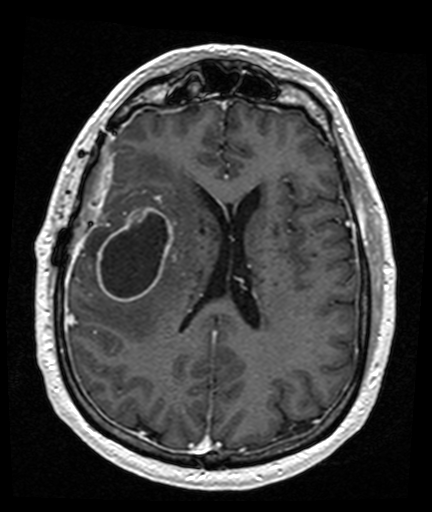
Brain MRI from a brain-tumour surgery series, one axial slice; slice 67 of 176 in the series (ordered by position); T1-weighted post-contrast; 1 mm slice thickness; 432 × 512 image matrix, field of view 194 × 230 mm. From the clinical record (not read from this slice): histopathology: Glioblastoma; WHO grade: 4; IDH mutation: no.
Annotated regions visible in this slice (outlined manually by an expert reader):
- tumour: bounding box (x1, y1, x2, y2) in pixels: (97, 206, 174, 302)